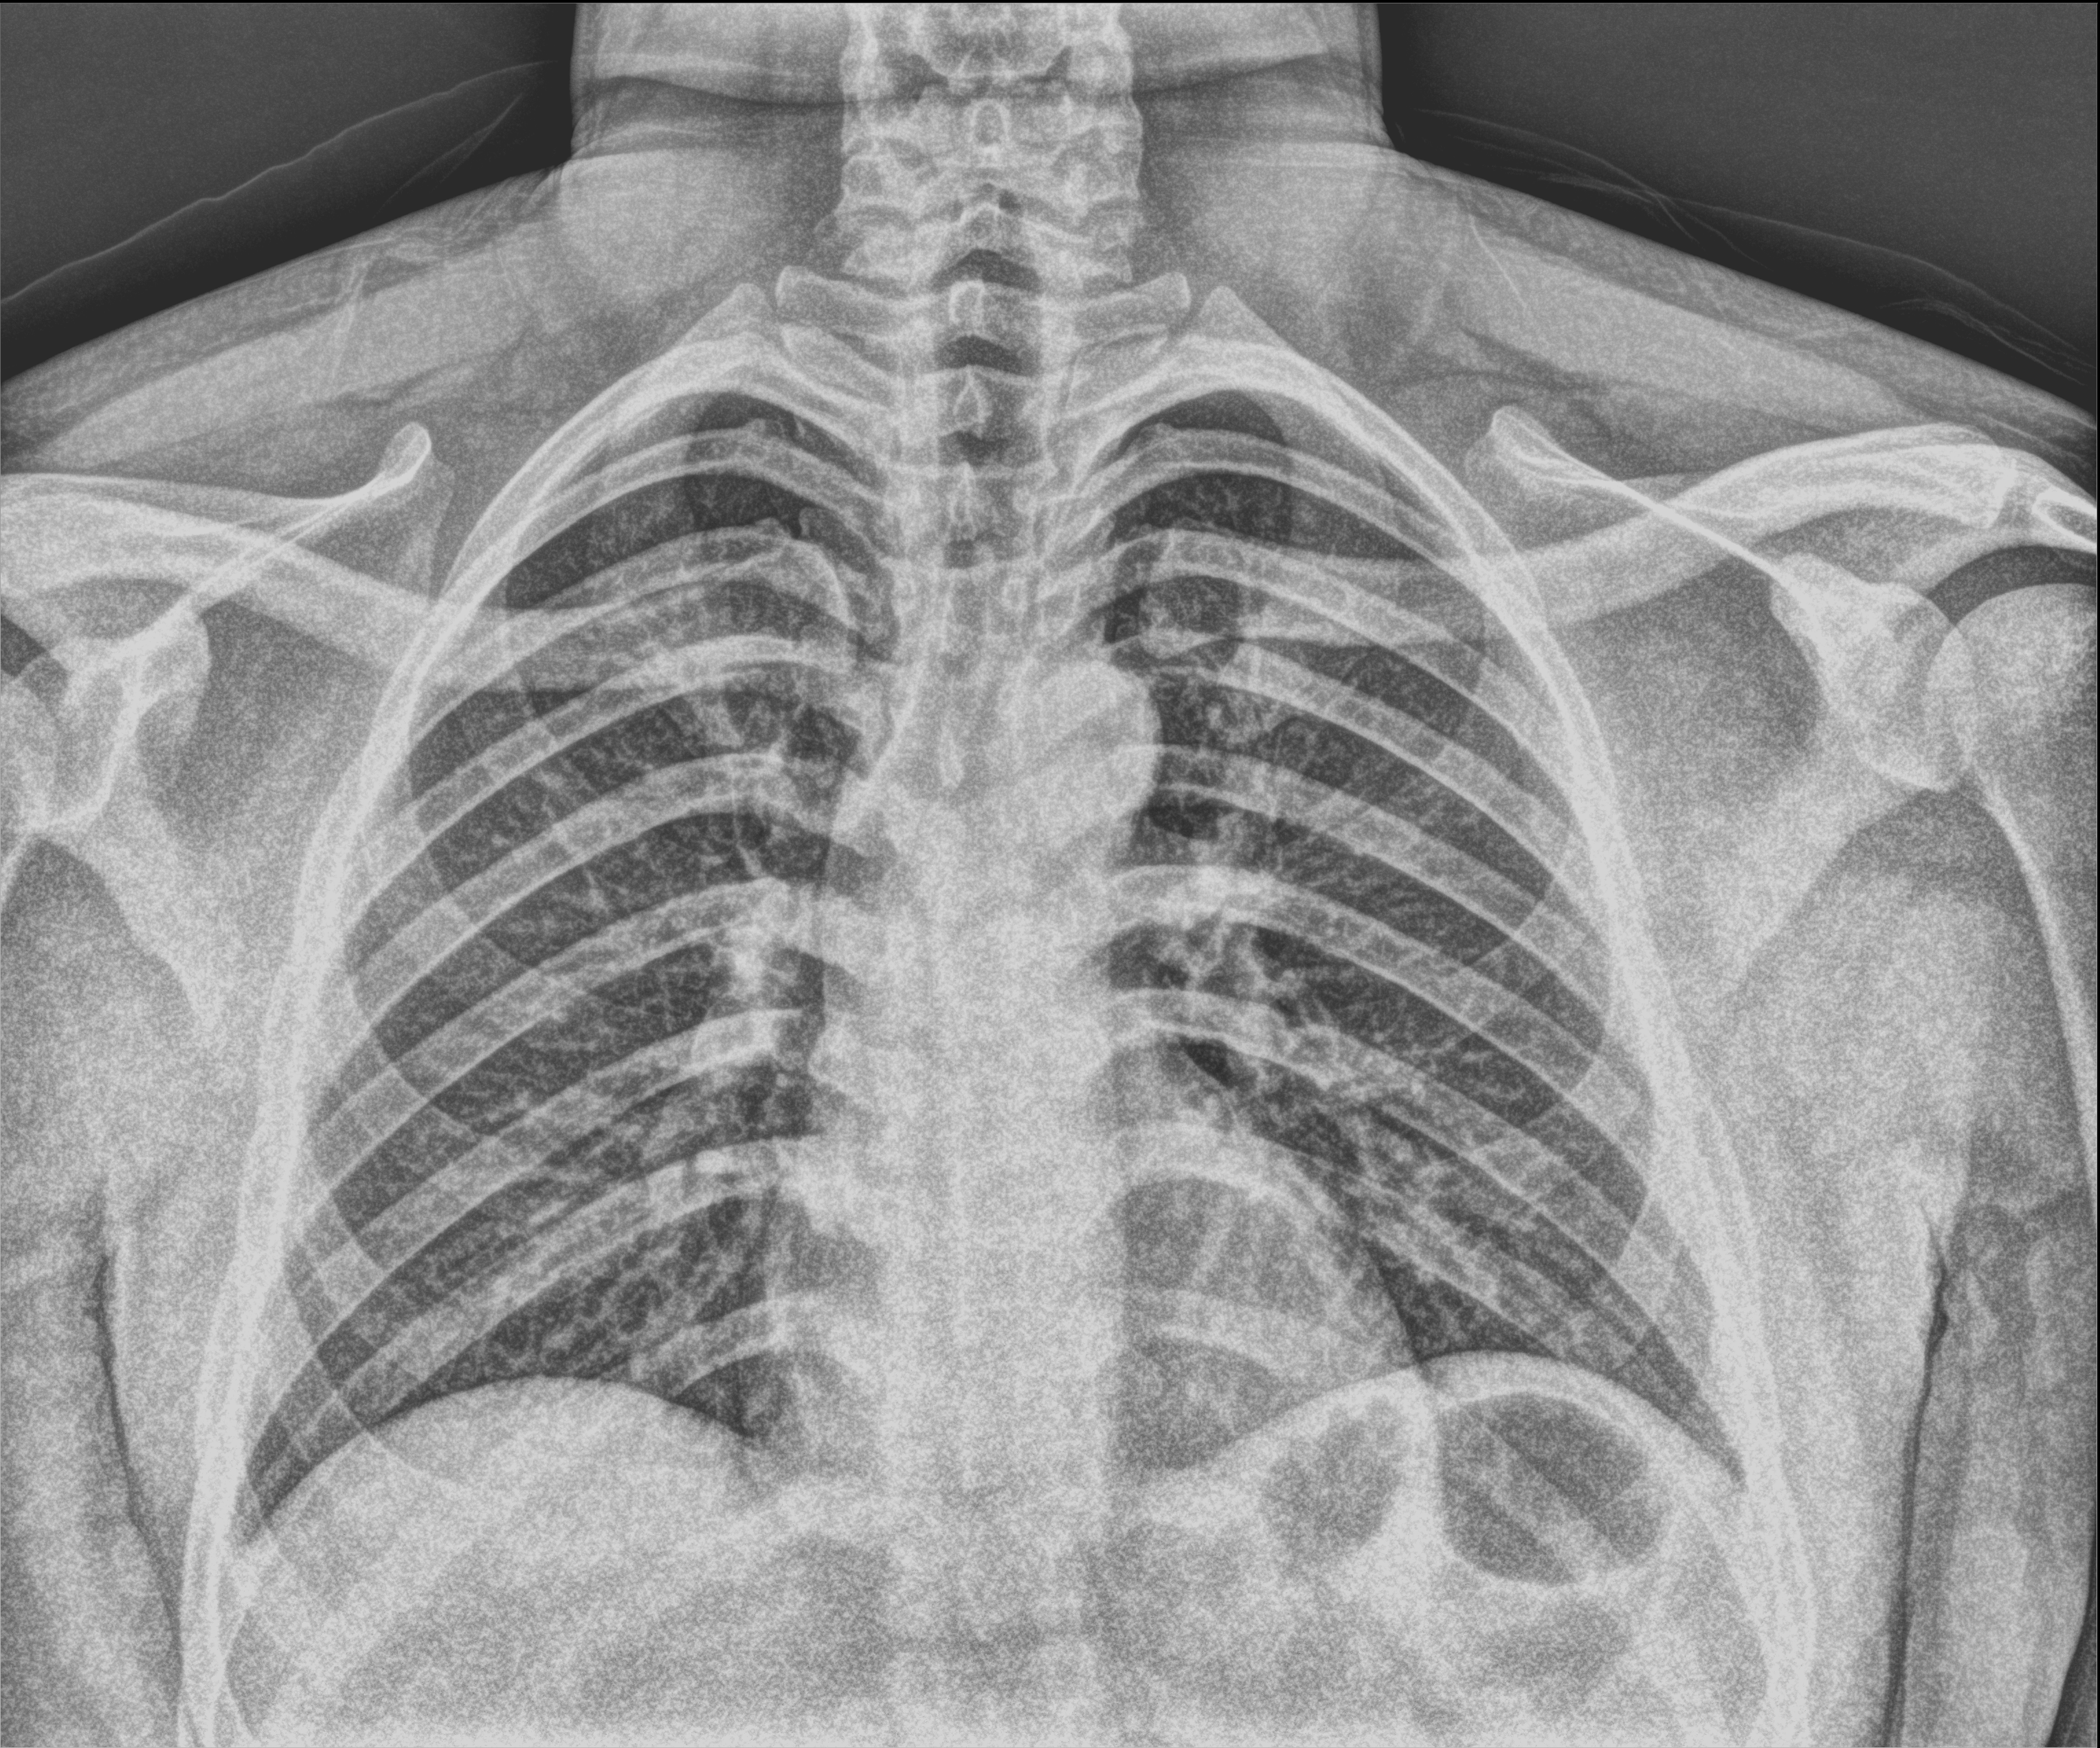
Bedside chest radiograph (computed radiography). Patient hospitalised with COVID-19; male, aged 18–59 years.
Admission-level facts for this patient (not findings on this image; timing relative to this image not recorded): length of hospital stay: 2 days.